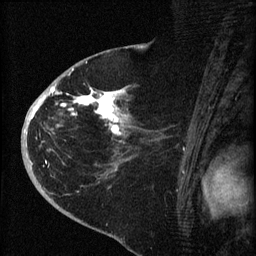
Breast MRI (dynamic contrast-enhanced), one sagittal slice. Position 40 of 60 along the scan axis. Dynamic contrast-enhanced series, image 2 of 4 at this slice position (ordered by acquisition). 1.5 T. TE 4.2 ms, TR 8.2 ms. 2 mm slice thickness. 256 × 256 image matrix, field of view 180 × 180 mm. Patient: female, 71 years.
Structures marked on this image (semi-automatically segmented with operator editing):
- analysis volume of interest (the breast-tissue region the enhancement analysis was run in; not a lesion): bounding box [x1, y1, x2, y2] px = [35, 75, 153, 190]
- tumour enhancement mask (voxels above the 70 % enhancement threshold inside the analysis volume of interest): [35, 85, 126, 135]